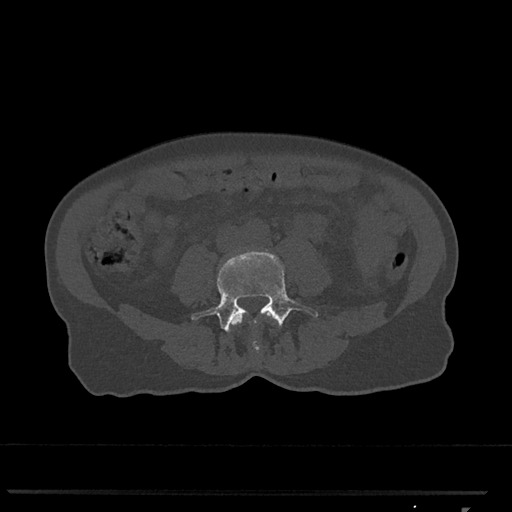
CT including the spine, one axial slice; position 225 of 793 along the scan axis; 120 kVp; bone window (W 1800 / L 400 HU); 0.5 mm slice thickness; 512 × 512 image matrix, field of view 380 × 380 mm. Patient: female, 62 years. From the clinical record (not read from this slice): primary cancer: renal.
Annotated regions visible in this slice (semi-automatically segmented with operator editing):
- L3 vertebra: box from (x=230, y=314) to (x=274, y=353) px
- L4 vertebra: (x=191, y=250)–(x=318, y=333)